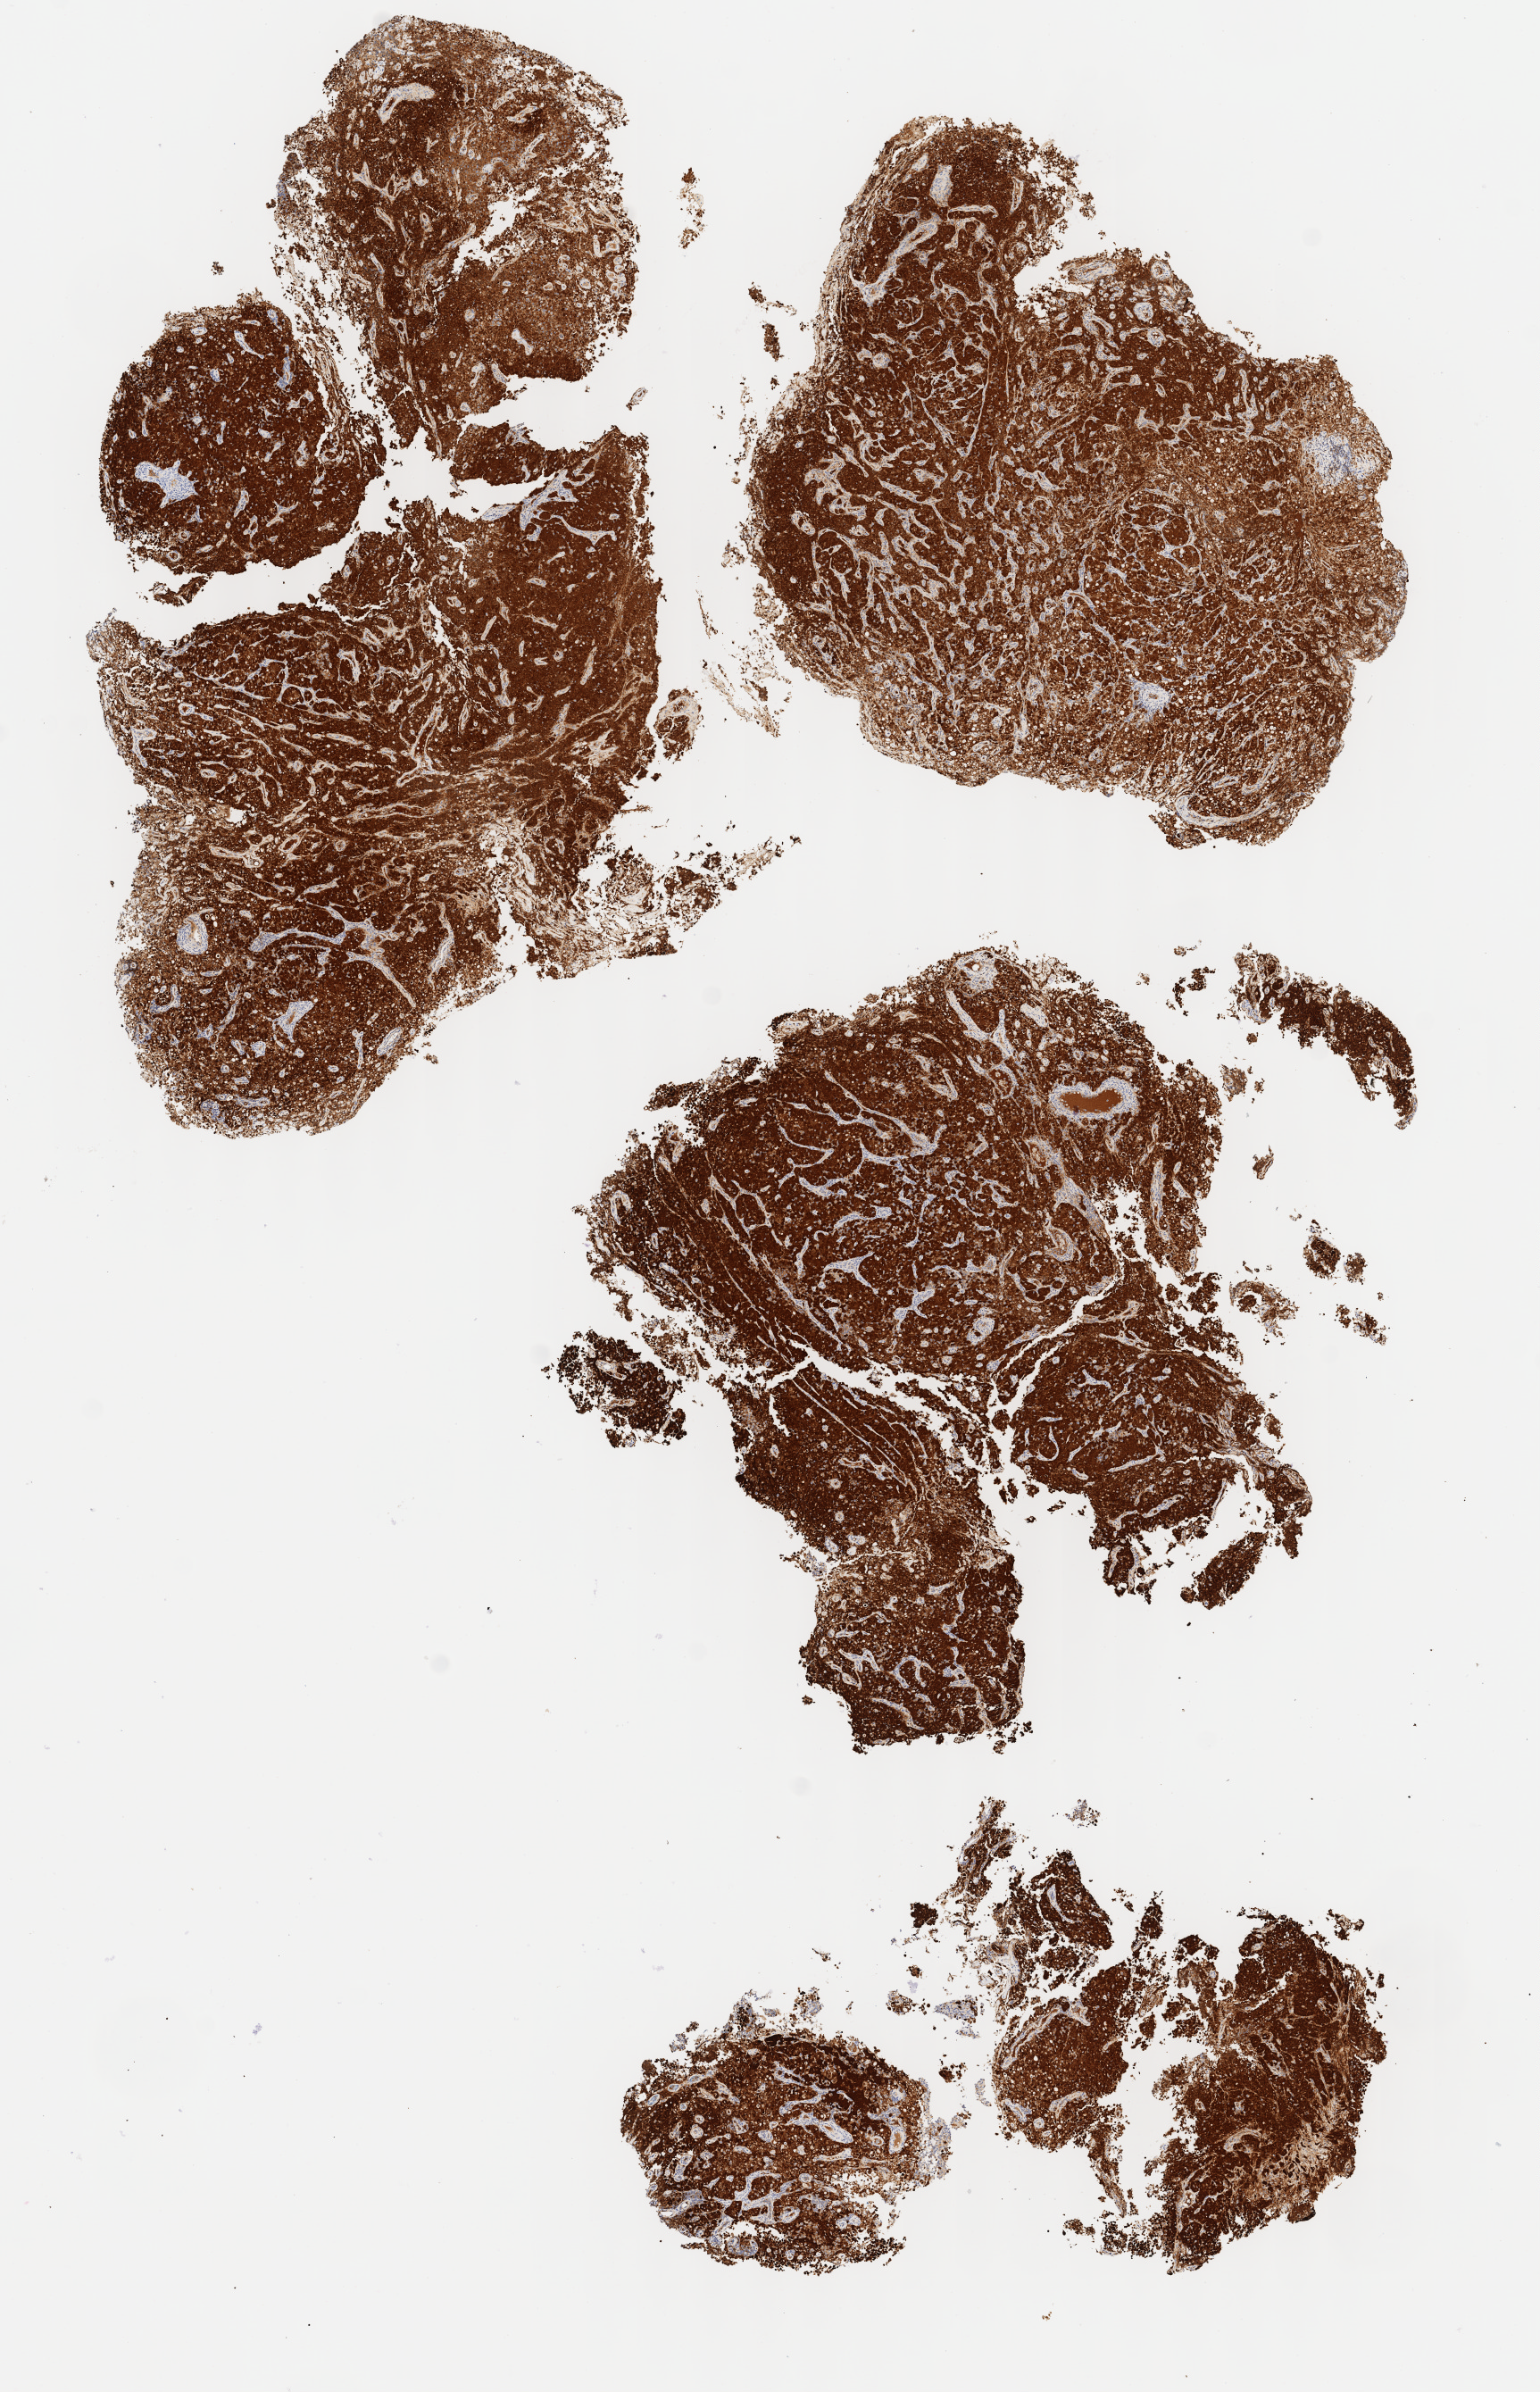
Immunohistochemistry (IHC) whole-slide image stained for p16 (p16INK4a) — low-resolution overview of the scanned area, about 6.9 x 10.7 mm; specimen: tumor tissue; anatomic site: cervix. Patient: female, age 75 years.
* histologic diagnosis: Adenocarcinoma, NOS